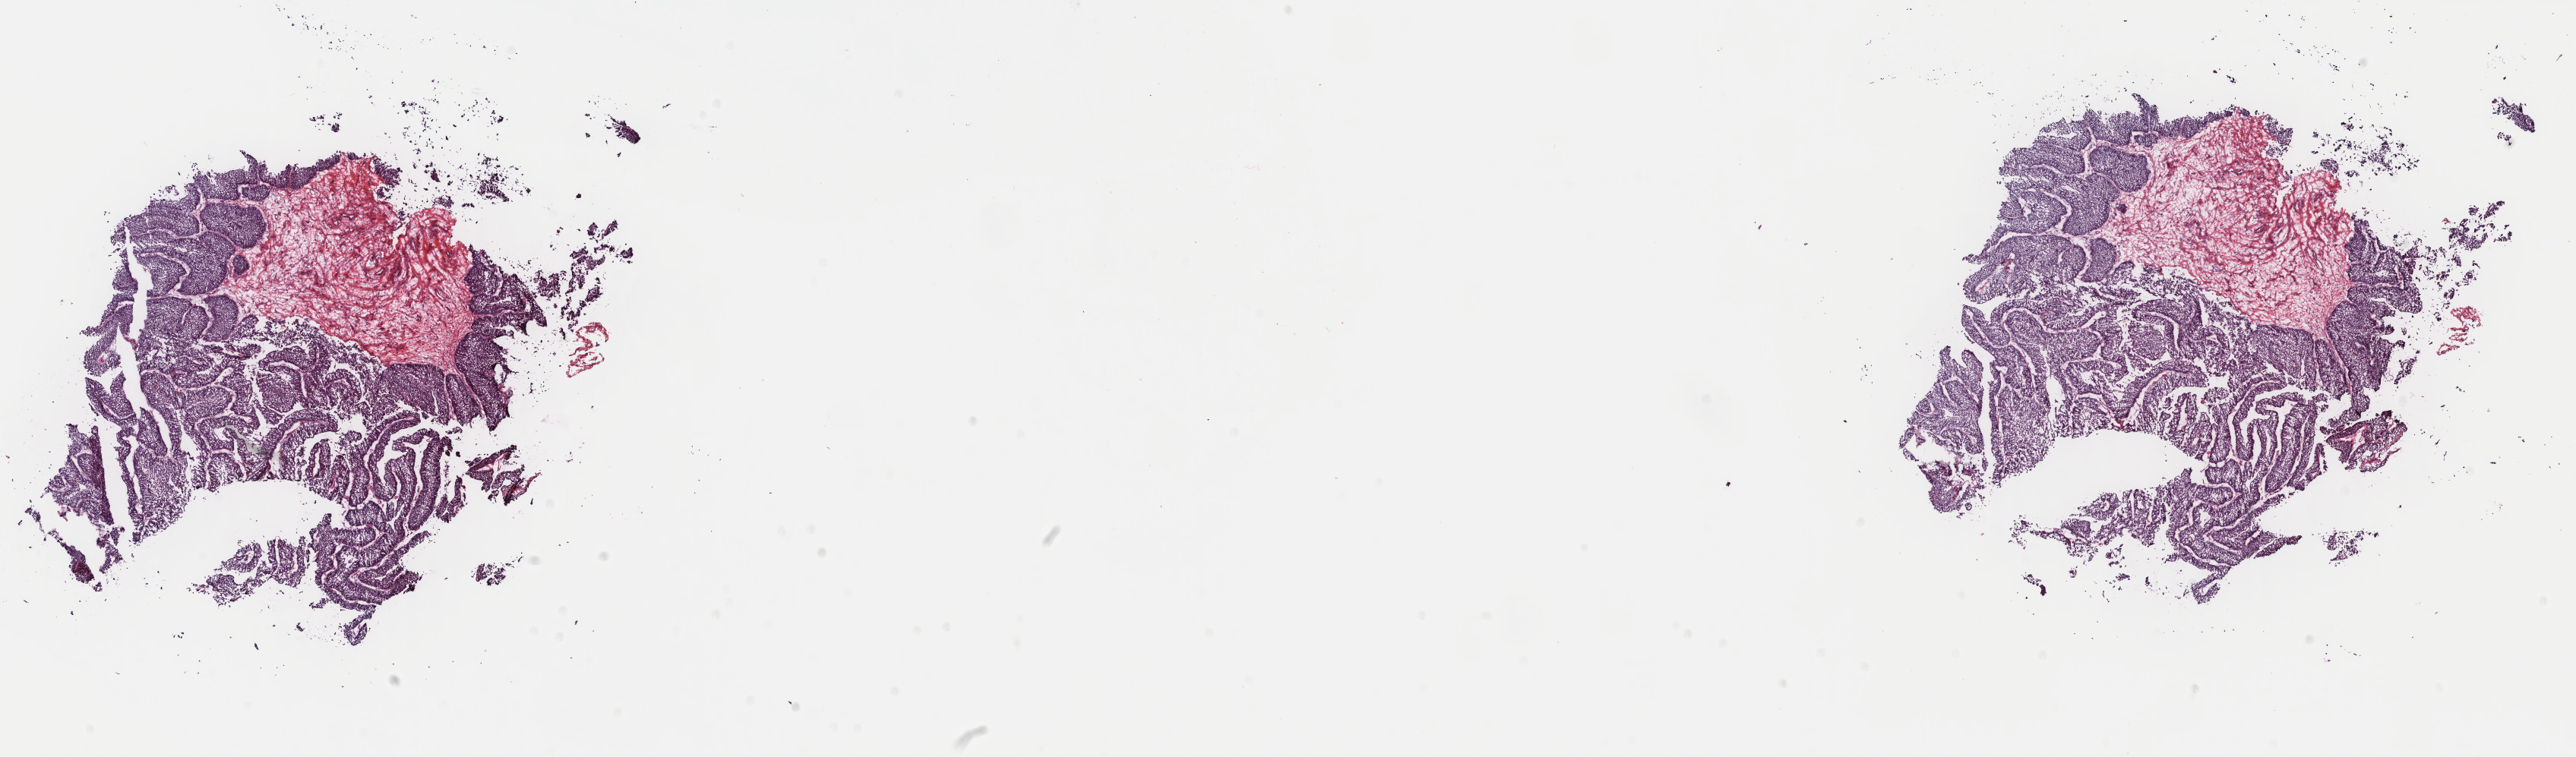
Digitized H&E tissue section (whole slide), whole scanned area (about 26.9 x 7.9 mm, slide scanned at 40x) shown as a low-resolution overview. Frozen section from the top of the tissue portion. Bladder, primary tumour sample. Patient: male, age at initial diagnosis 72 years. Histologic grade: high grade. Composition of this section per pathologist review: tumour cells 70%, tumour nuclei 80%, normal cells 0%, stromal cells 30%, necrosis 0%. Inflammatory infiltration, as recorded: lymphocyte infiltration 0%, monocyte infiltration 0%, neutrophil infiltration 0%.
Histologic diagnosis: Transitional cell carcinoma (lateral wall of bladder). AJCC pathologic stage: III. TNM: T4 N0 M0.